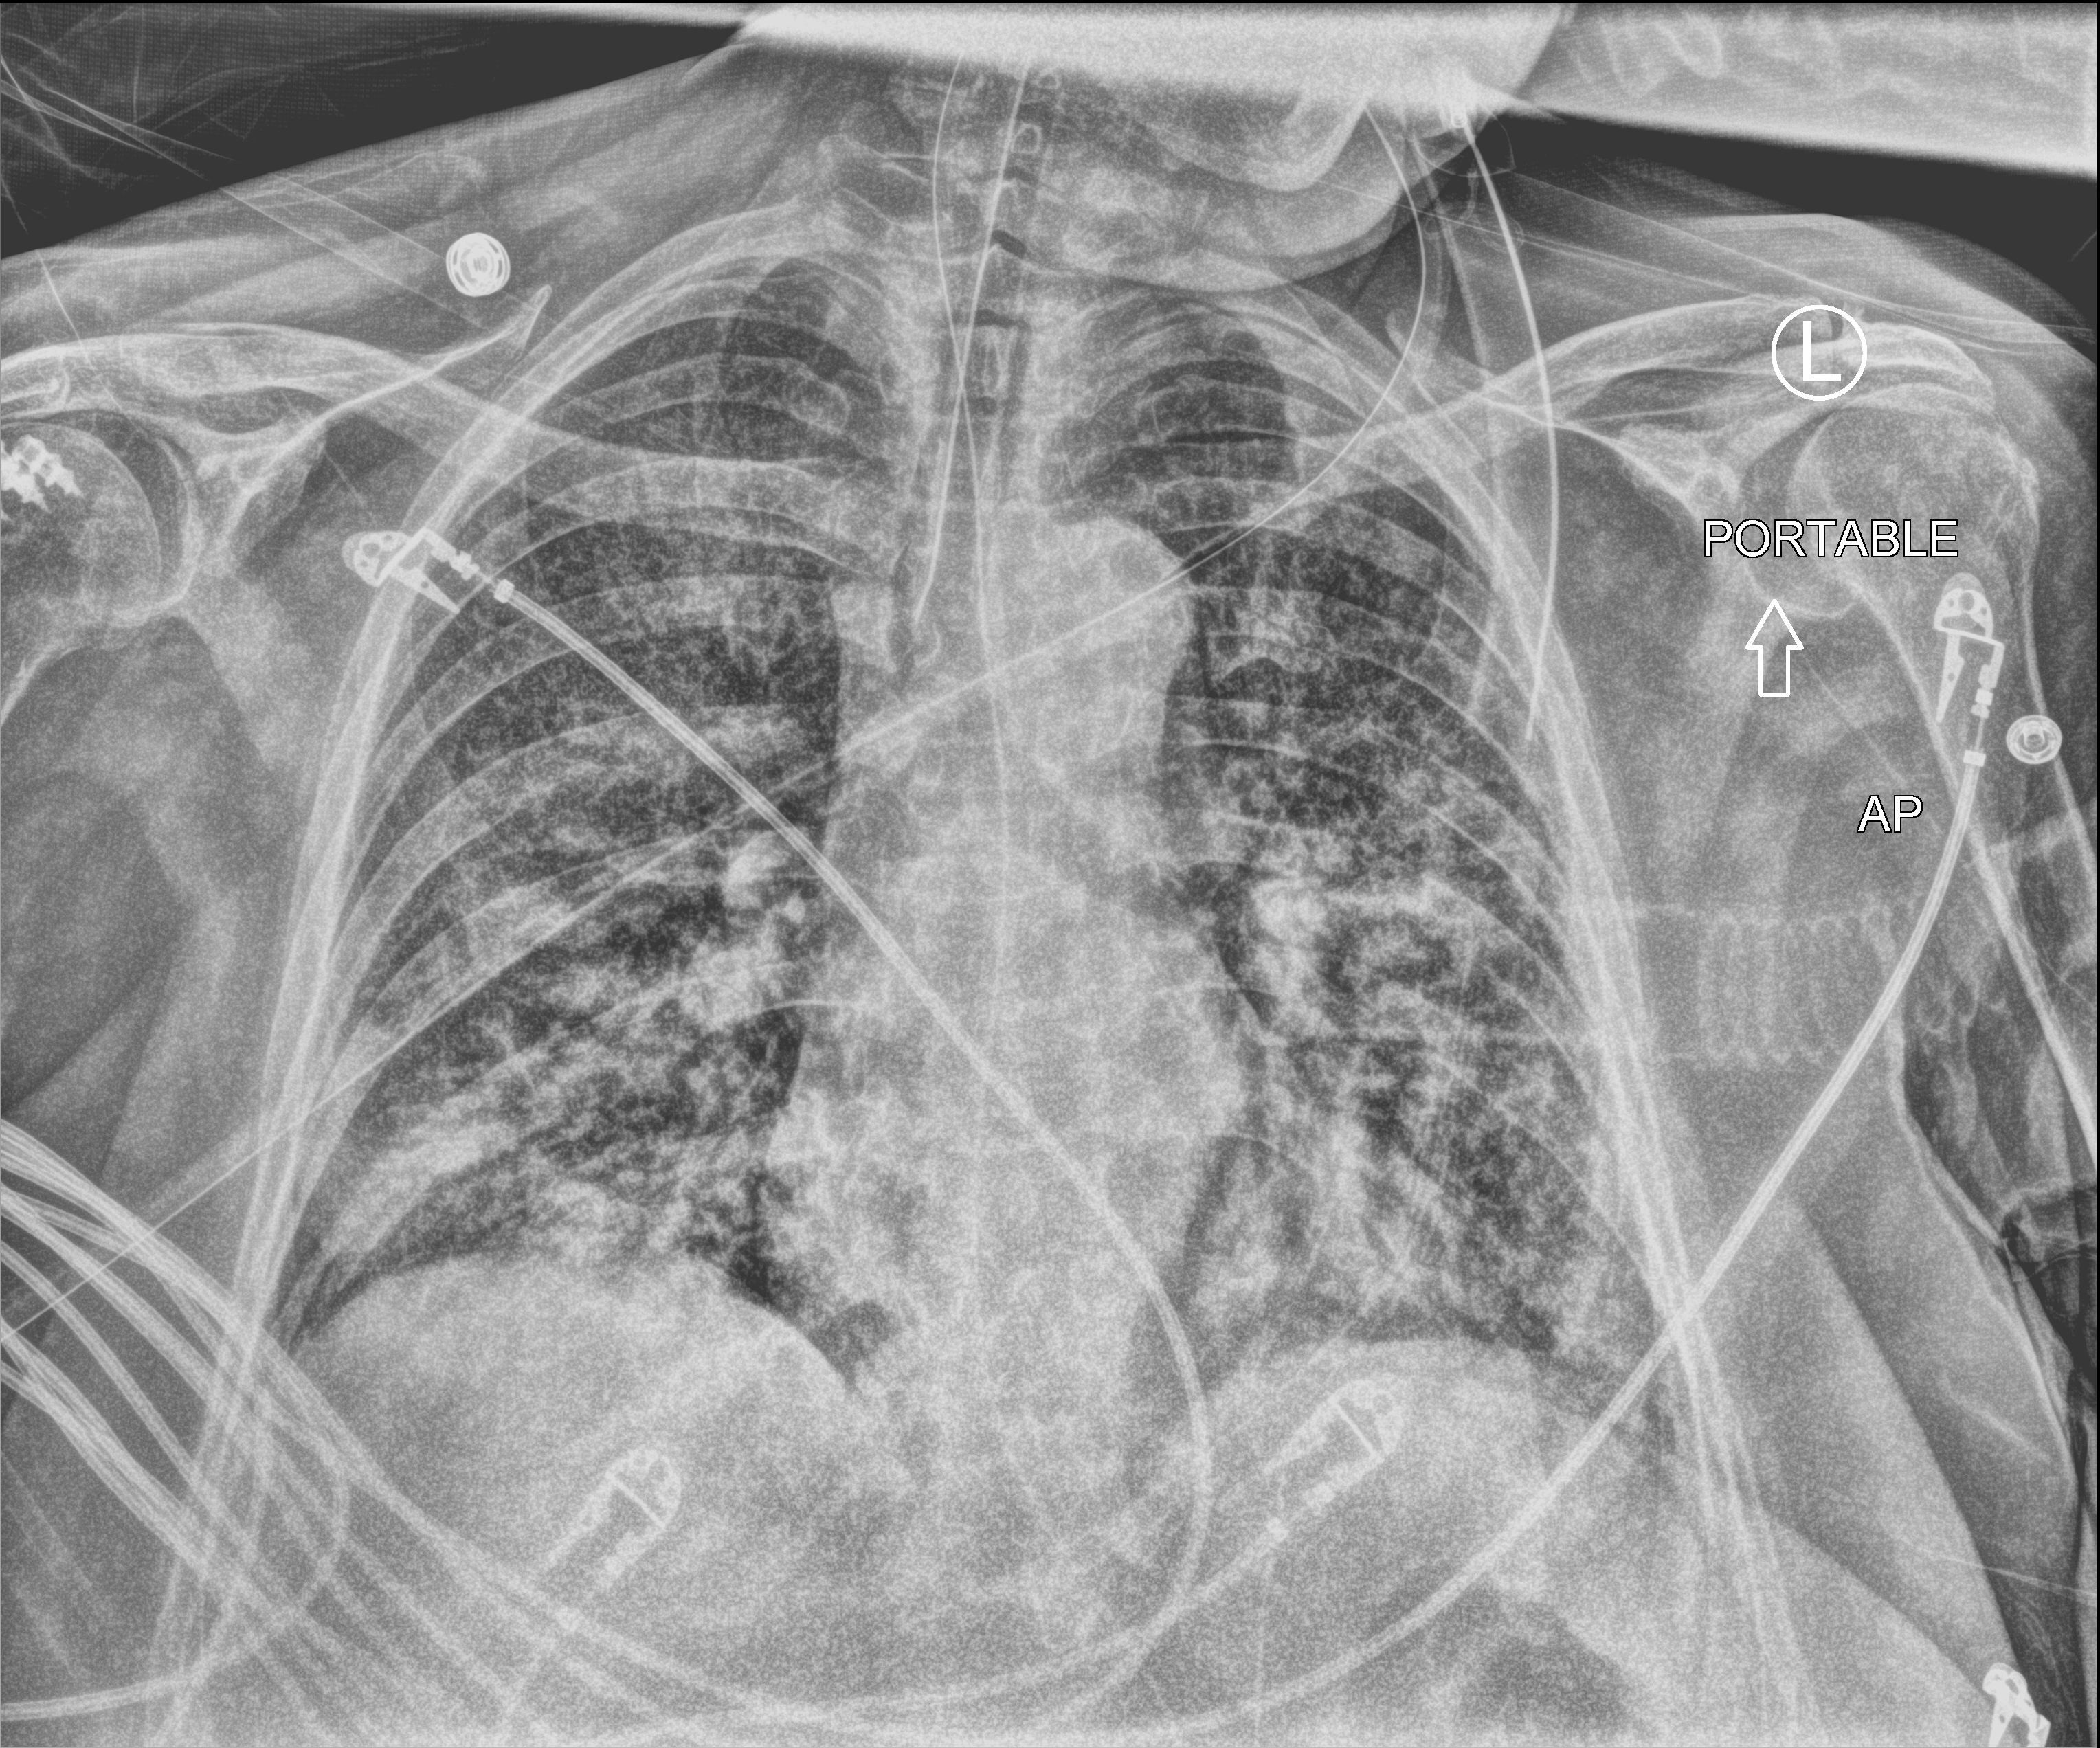
Portable chest radiograph. Patient hospitalised with COVID-19; female, aged 60–74 years.
Admission-level facts for this patient (not findings on this image; timing relative to this image not recorded):
- admitted to intensive care during this hospital stay: yes
- mechanically ventilated during this hospital stay: yes